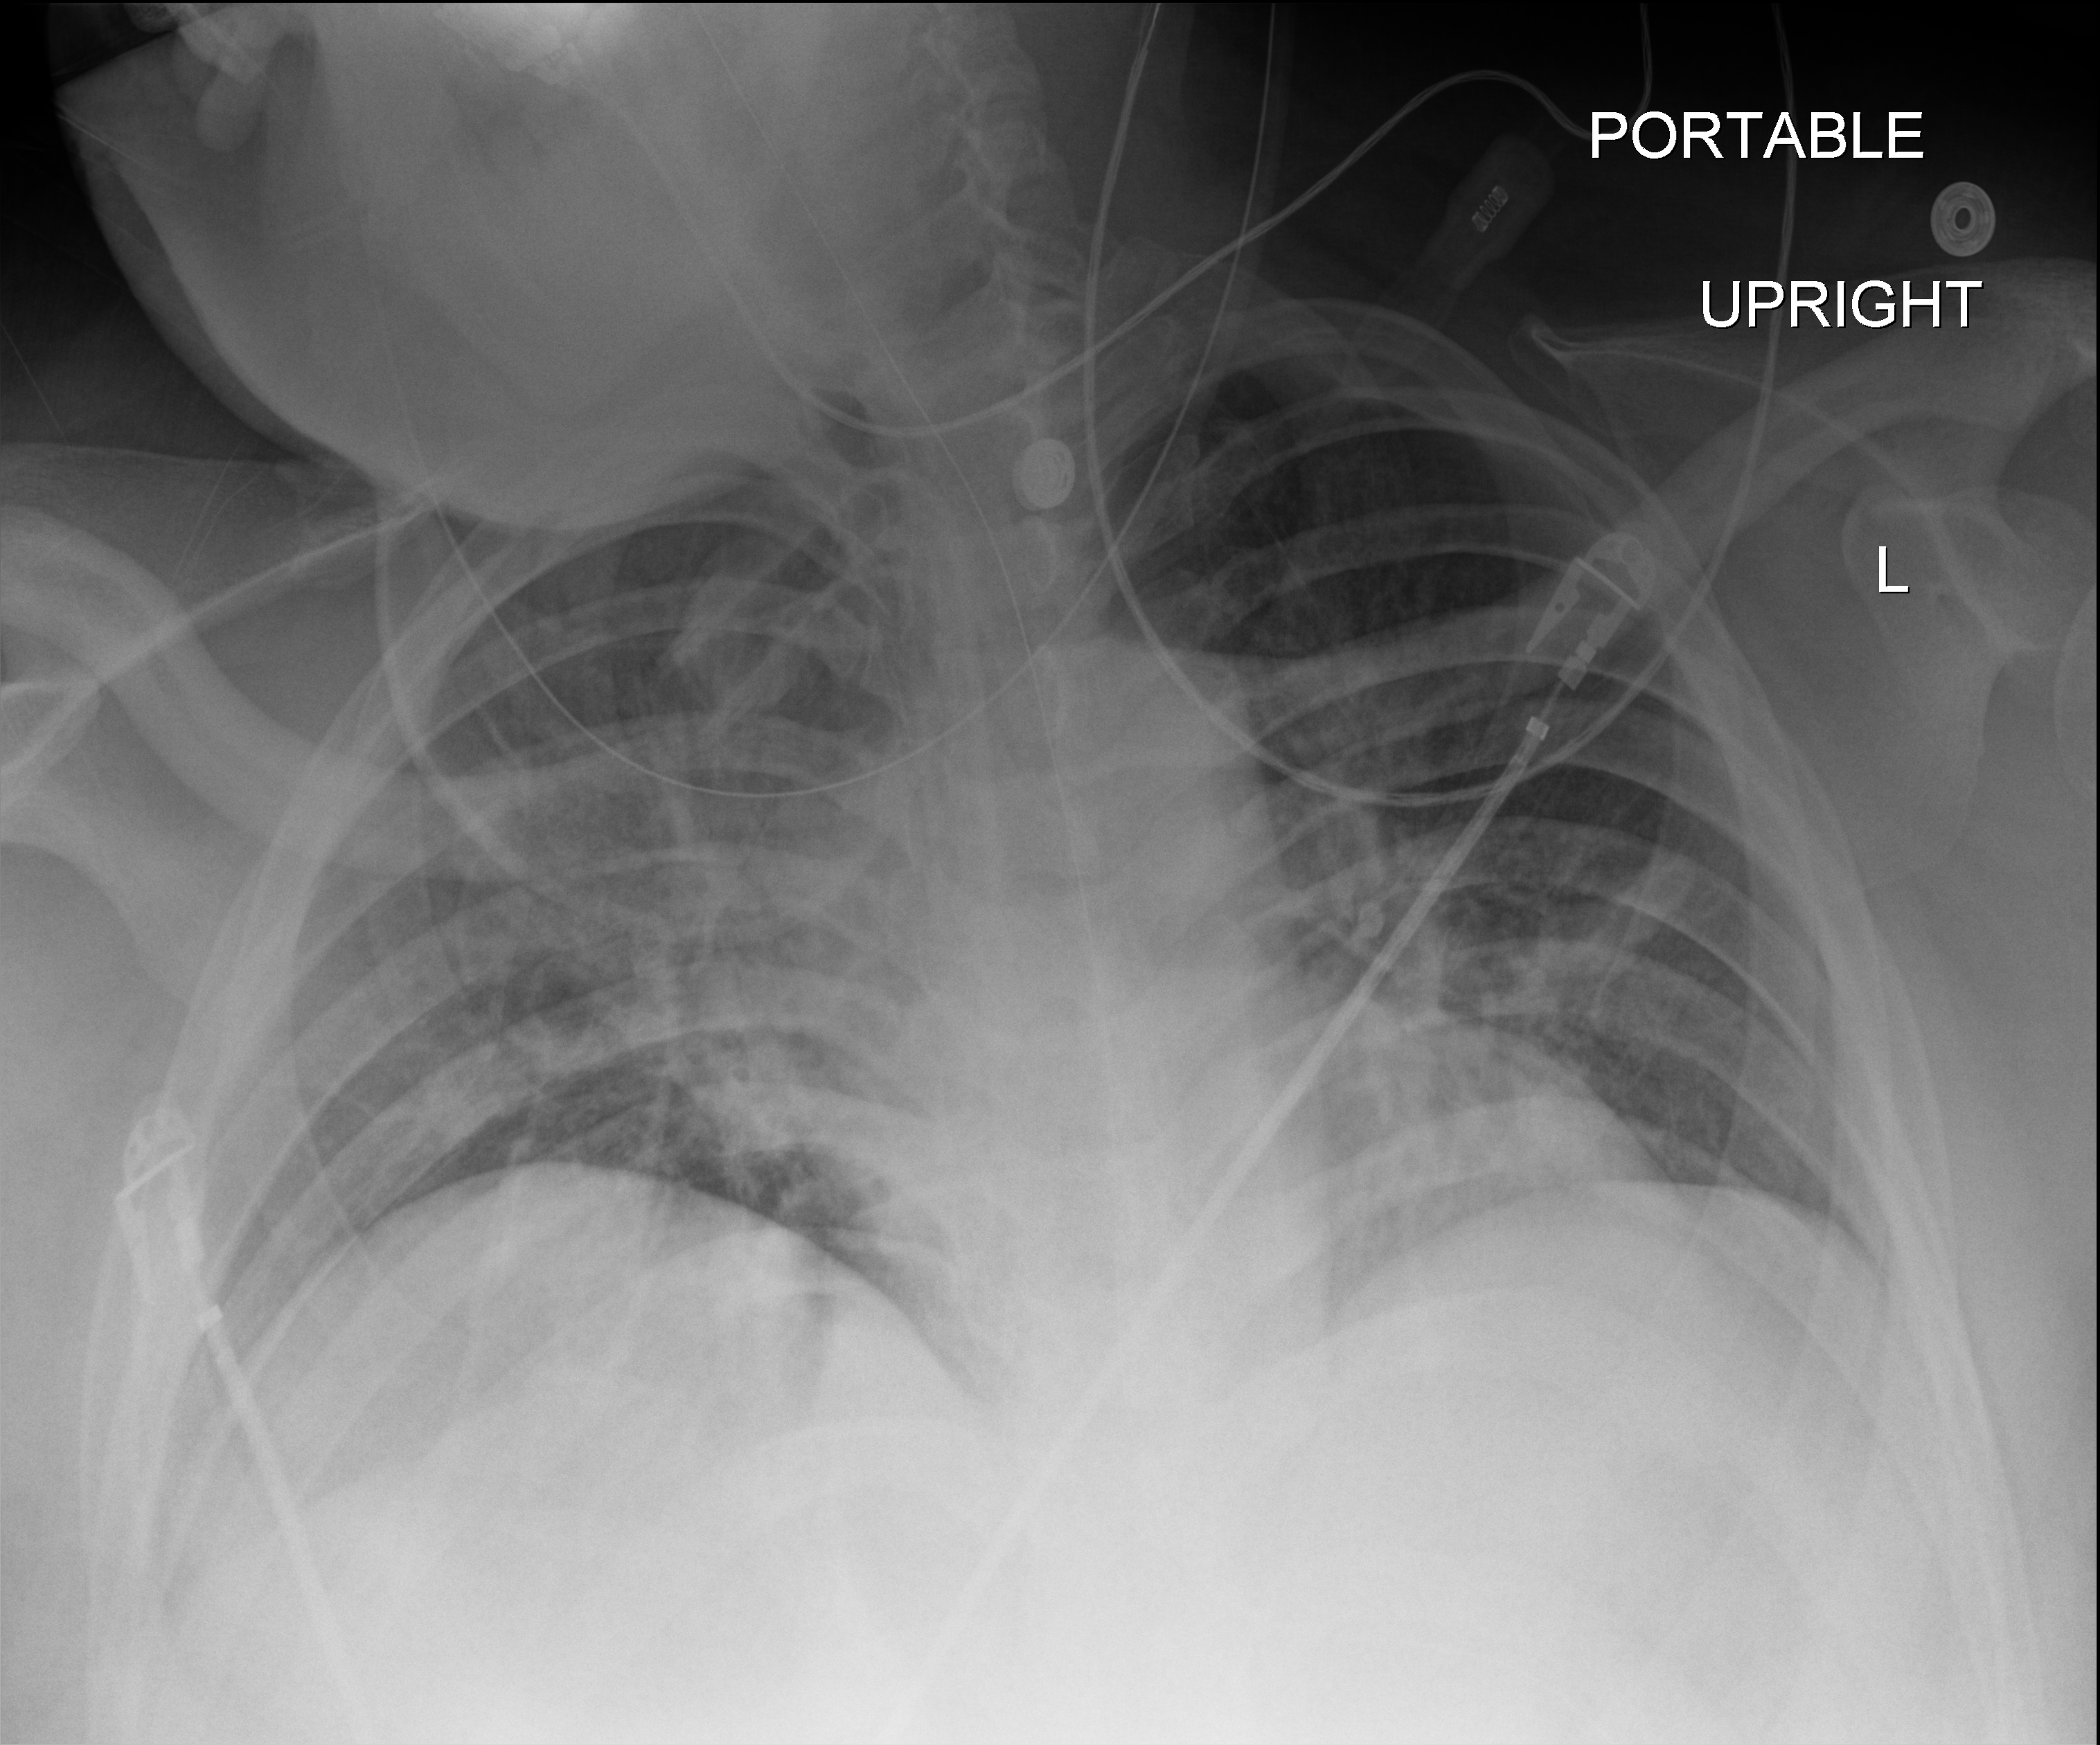
Bedside chest radiograph (digital radiography); anteroposterior (AP) projection. Patient hospitalised with COVID-19; male, aged 18–59 years.
From the hospital-stay record, not from the radiograph (when in the stay this image was taken is not recorded):
- mechanically ventilated during this hospital stay: yes